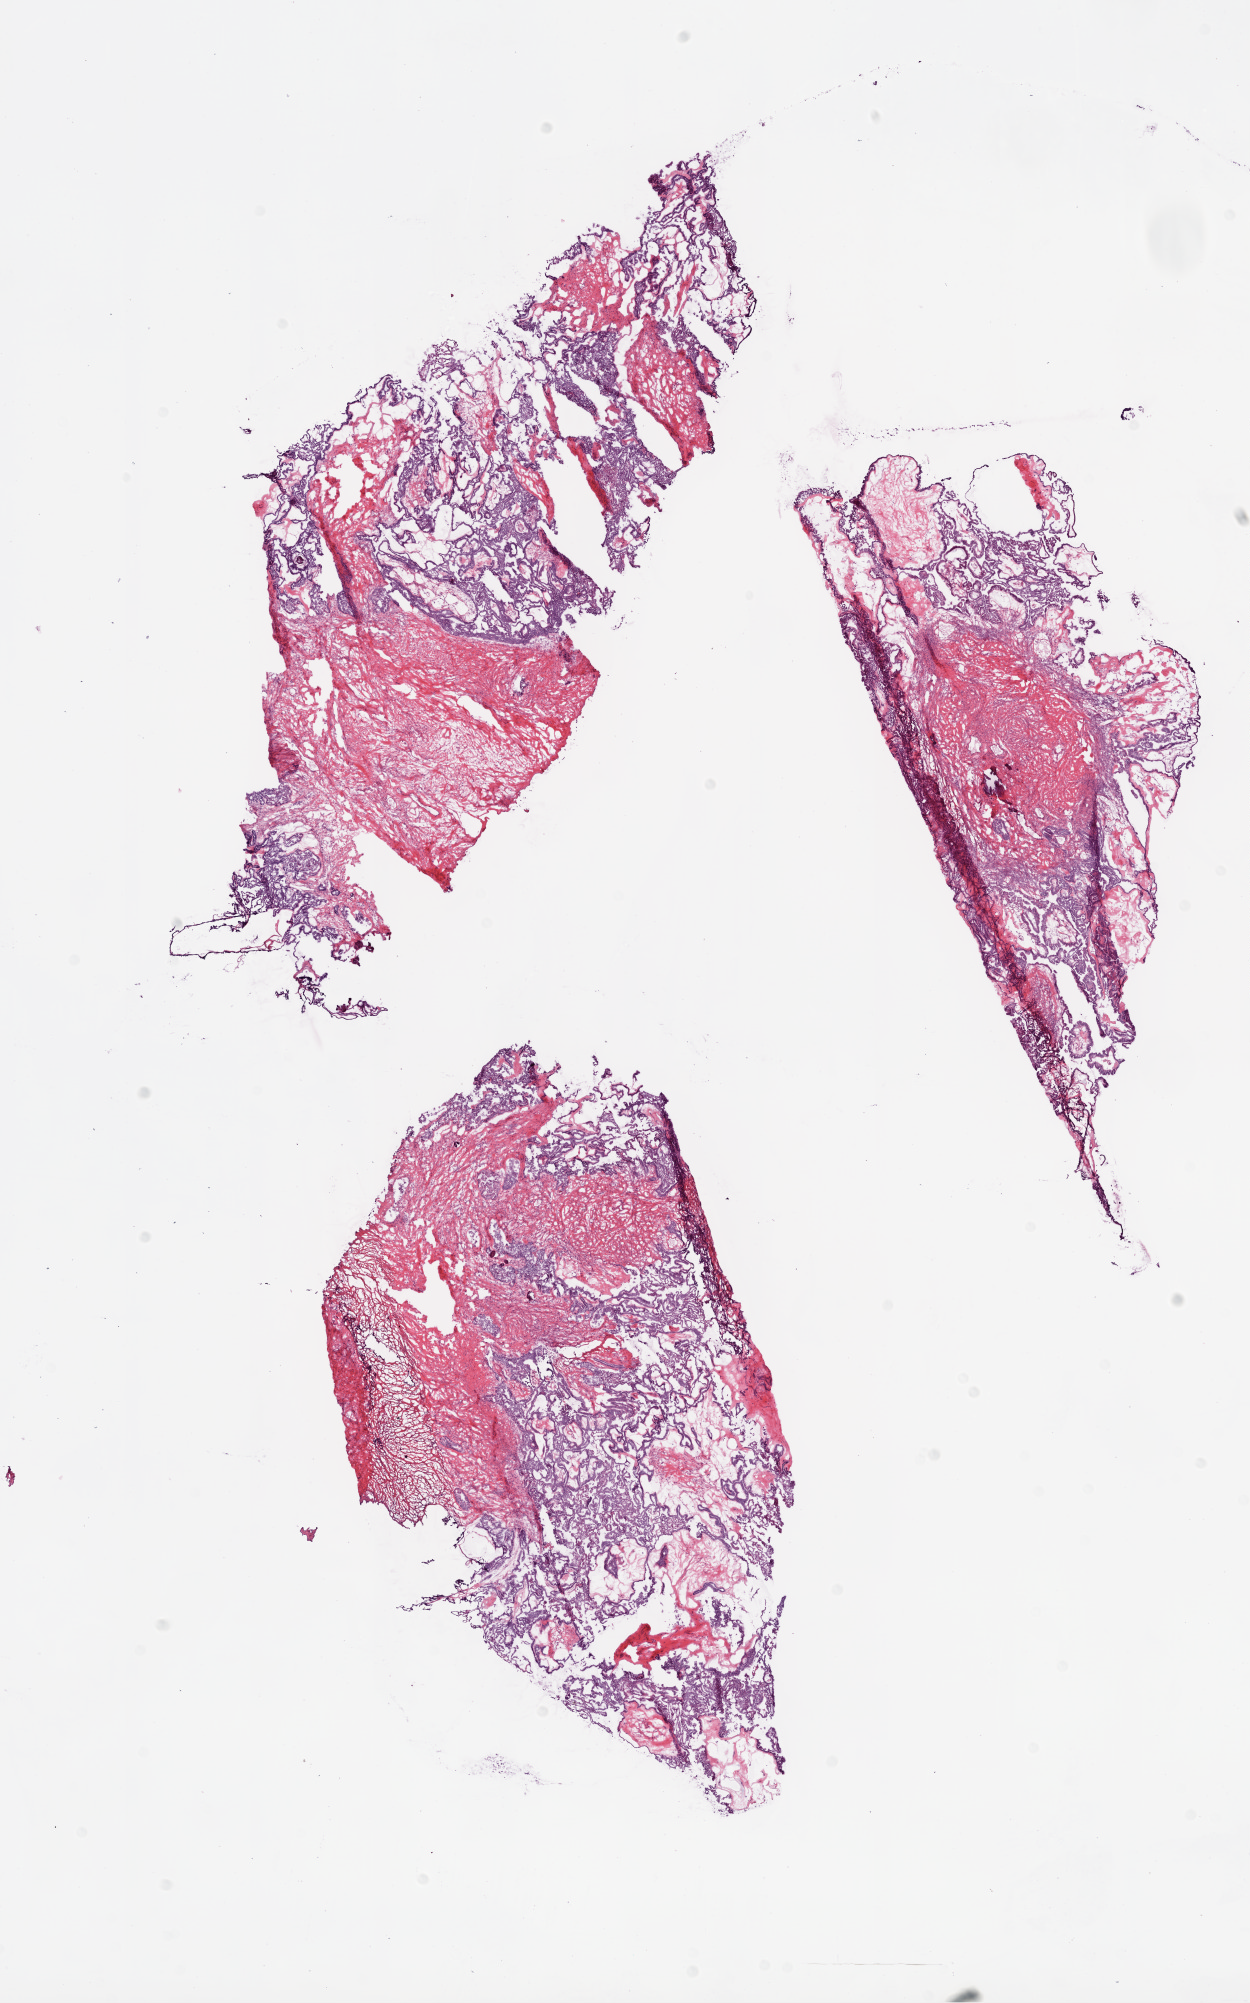
Digitized Hematoxylin and eosin (H&E) stained tissue section (whole slide), shown as a low-resolution overview of the whole scanned area (about 10.0 x 16.1 mm); frozen section from the bottom of the tissue portion; sample: primary tumour, ovary. Female, age 68 years at initial diagnosis. Histologic grade: GB (borderline). Pathologist review of this section (percent, as recorded): tumour cells 60%, tumour nuclei 90%, normal cells 0%, stromal cells 40%, necrosis 0%. Inflammatory infiltration, as recorded: lymphocyte infiltration 2%, monocyte infiltration 0%, neutrophil infiltration 0%.
Pathologic diagnosis: Serous cystadenocarcinoma, NOS. Laterality: right. FIGO stage: IIIA.